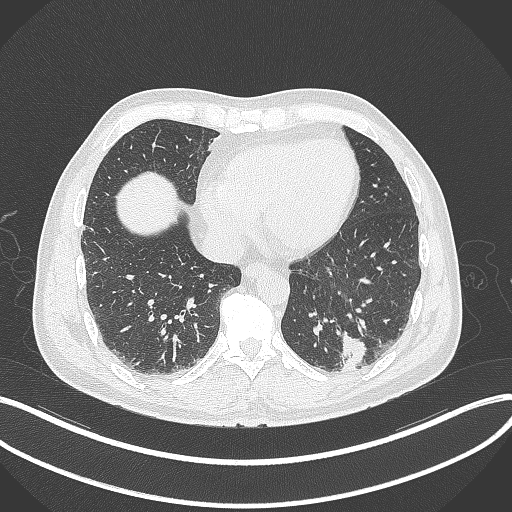
Chest CT, one axial slice. Slice 86 of 300 in the series (ordered by position). Reconstruction kernel B70f. Lung window (W 1500 / L -600 HU). 1 mm slice thickness. 512 × 512 image matrix. Patient: male, 54 years. From the clinical record (not read from this slice): clinical TNM (as recorded): T1c N0 M1; histopathological grade: G3.
Annotated regions visible in this slice (rectangle marked by the reading radiologist):
- lung tumour (recorded histology: adenocarcinoma): box from (x=337, y=331) to (x=370, y=371) px